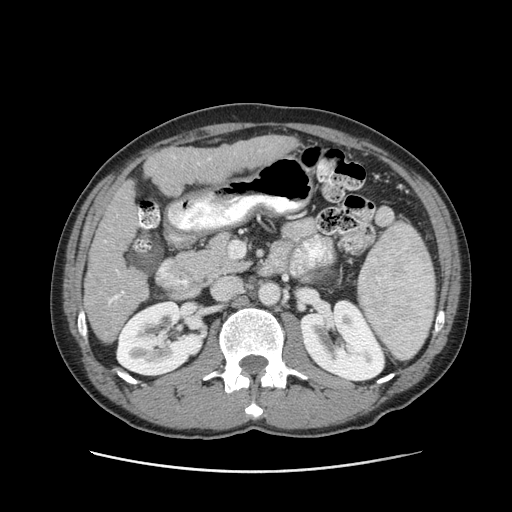
Contrast-enhanced abdominal CT (liver protocol), one axial slice; position 39 of 93 along the scan axis; reconstruction kernel STANDARD; 120 kVp; soft-tissue window (W 400 / L 40 HU); 2.5 mm slice thickness; 512 × 512 image matrix, field of view 380 × 380 mm. Case-level facts recorded for this patient, not image findings: diagnosis: hepatocellular carcinoma (patient treated with transarterial chemoembolisation; whether this scan precedes or follows treatment is not stated here); TNM stage (as recorded): Stage-II; Child-Pugh class: A; tumour size: 1 cm.
Annotated regions visible in this slice (semi-automatically segmented with operator editing):
- liver parenchyma outside the tumour (the mass and vessels are separate outlines, so this box may not span the whole liver): box from (x=84, y=134) to (x=298, y=342) px
- liver vessels: (x=105, y=157)–(x=210, y=305)